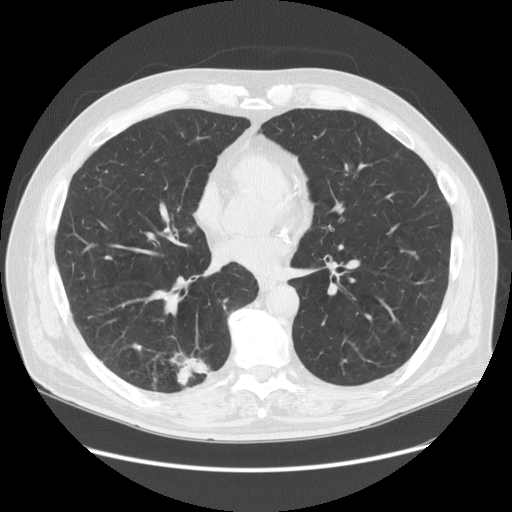
Low-dose screening chest CT, one axial slice. Position 67 of 149 along the scan axis. Lung window (W 1500 / L -600 HU). 2.5 mm slice thickness. 512 × 512 image matrix.
Structures marked on this image (outlined manually by an expert reader):
- lesion 1 (tumor, lower lobe of right lung): bounding box (x1, y1, x2, y2) in pixels: (176, 357, 212, 386)